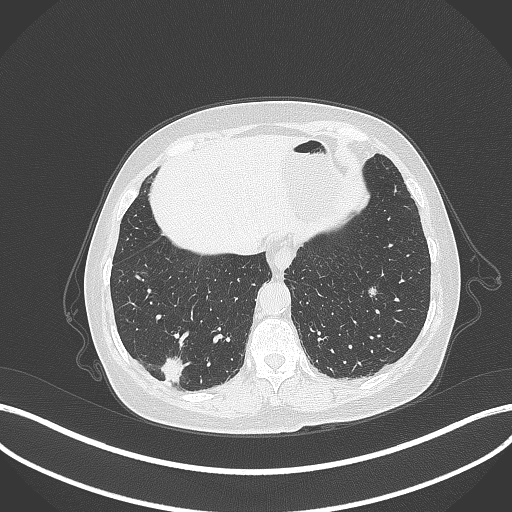
Chest CT, one axial slice. Slice 62 of 333 in the series (ordered by position). 120 kVp. Lung window (W 1500 / L -600 HU). 1 mm slice thickness. 512 × 512 image matrix, field of view 400 × 400 mm. Patient: female, 69 years. From the clinical record (not read from this slice): clinical TNM (as recorded): T1b N0 M0; histopathological grade: G2-3.
Structures marked on this image (rectangle marked by the reading radiologist):
- lung tumour (recorded histology: adenocarcinoma): bounding box <156,353,187,385> (left, top, right, bottom; pixels)